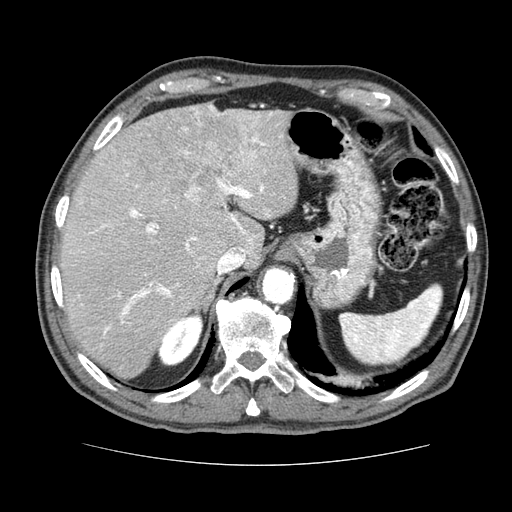
Contrast-enhanced abdominal CT (liver protocol), one axial slice. Position 53 of 79 along the scan axis. Reconstruction kernel STANDARD. 120 kVp. Soft-tissue window (W 400 / L 40 HU). 2.5 mm slice thickness. 512 × 512 image matrix. Case-level facts recorded for this patient, not image findings: diagnosis: hepatocellular carcinoma (patient treated with transarterial chemoembolisation; whether this scan precedes or follows treatment is not stated here); TNM stage (as recorded): Stage-I; Child-Pugh class: A.
Outlined on this slice (semi-automatically segmented with operator editing):
- liver parenchyma outside the tumour (the mass and vessels are separate outlines, so this box may not span the whole liver): bounding box <60,102,298,378> (left, top, right, bottom; pixels)
- mass: <133,103,259,209>
- liver vessels: <78,113,272,334>